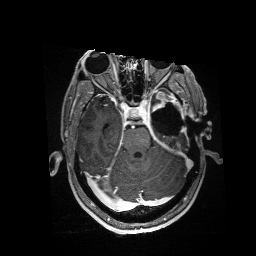
Brain MRI from a brain-tumour surgery series, one axial slice; position 109 of 176 along the scan axis; T1-weighted post-contrast; 1 mm slice thickness; 256 × 256 image matrix, field of view 256 × 256 mm. From the clinical record (not read from this slice): histopathology: Glioblastoma; WHO grade: 4; IDH mutation: no; tumour location: Left Anterior/Superior Temporal.
Outlined on this slice (outlined manually by an expert reader):
- residual tumour: bounding box [x1, y1, x2, y2] px = [153, 92, 185, 119]